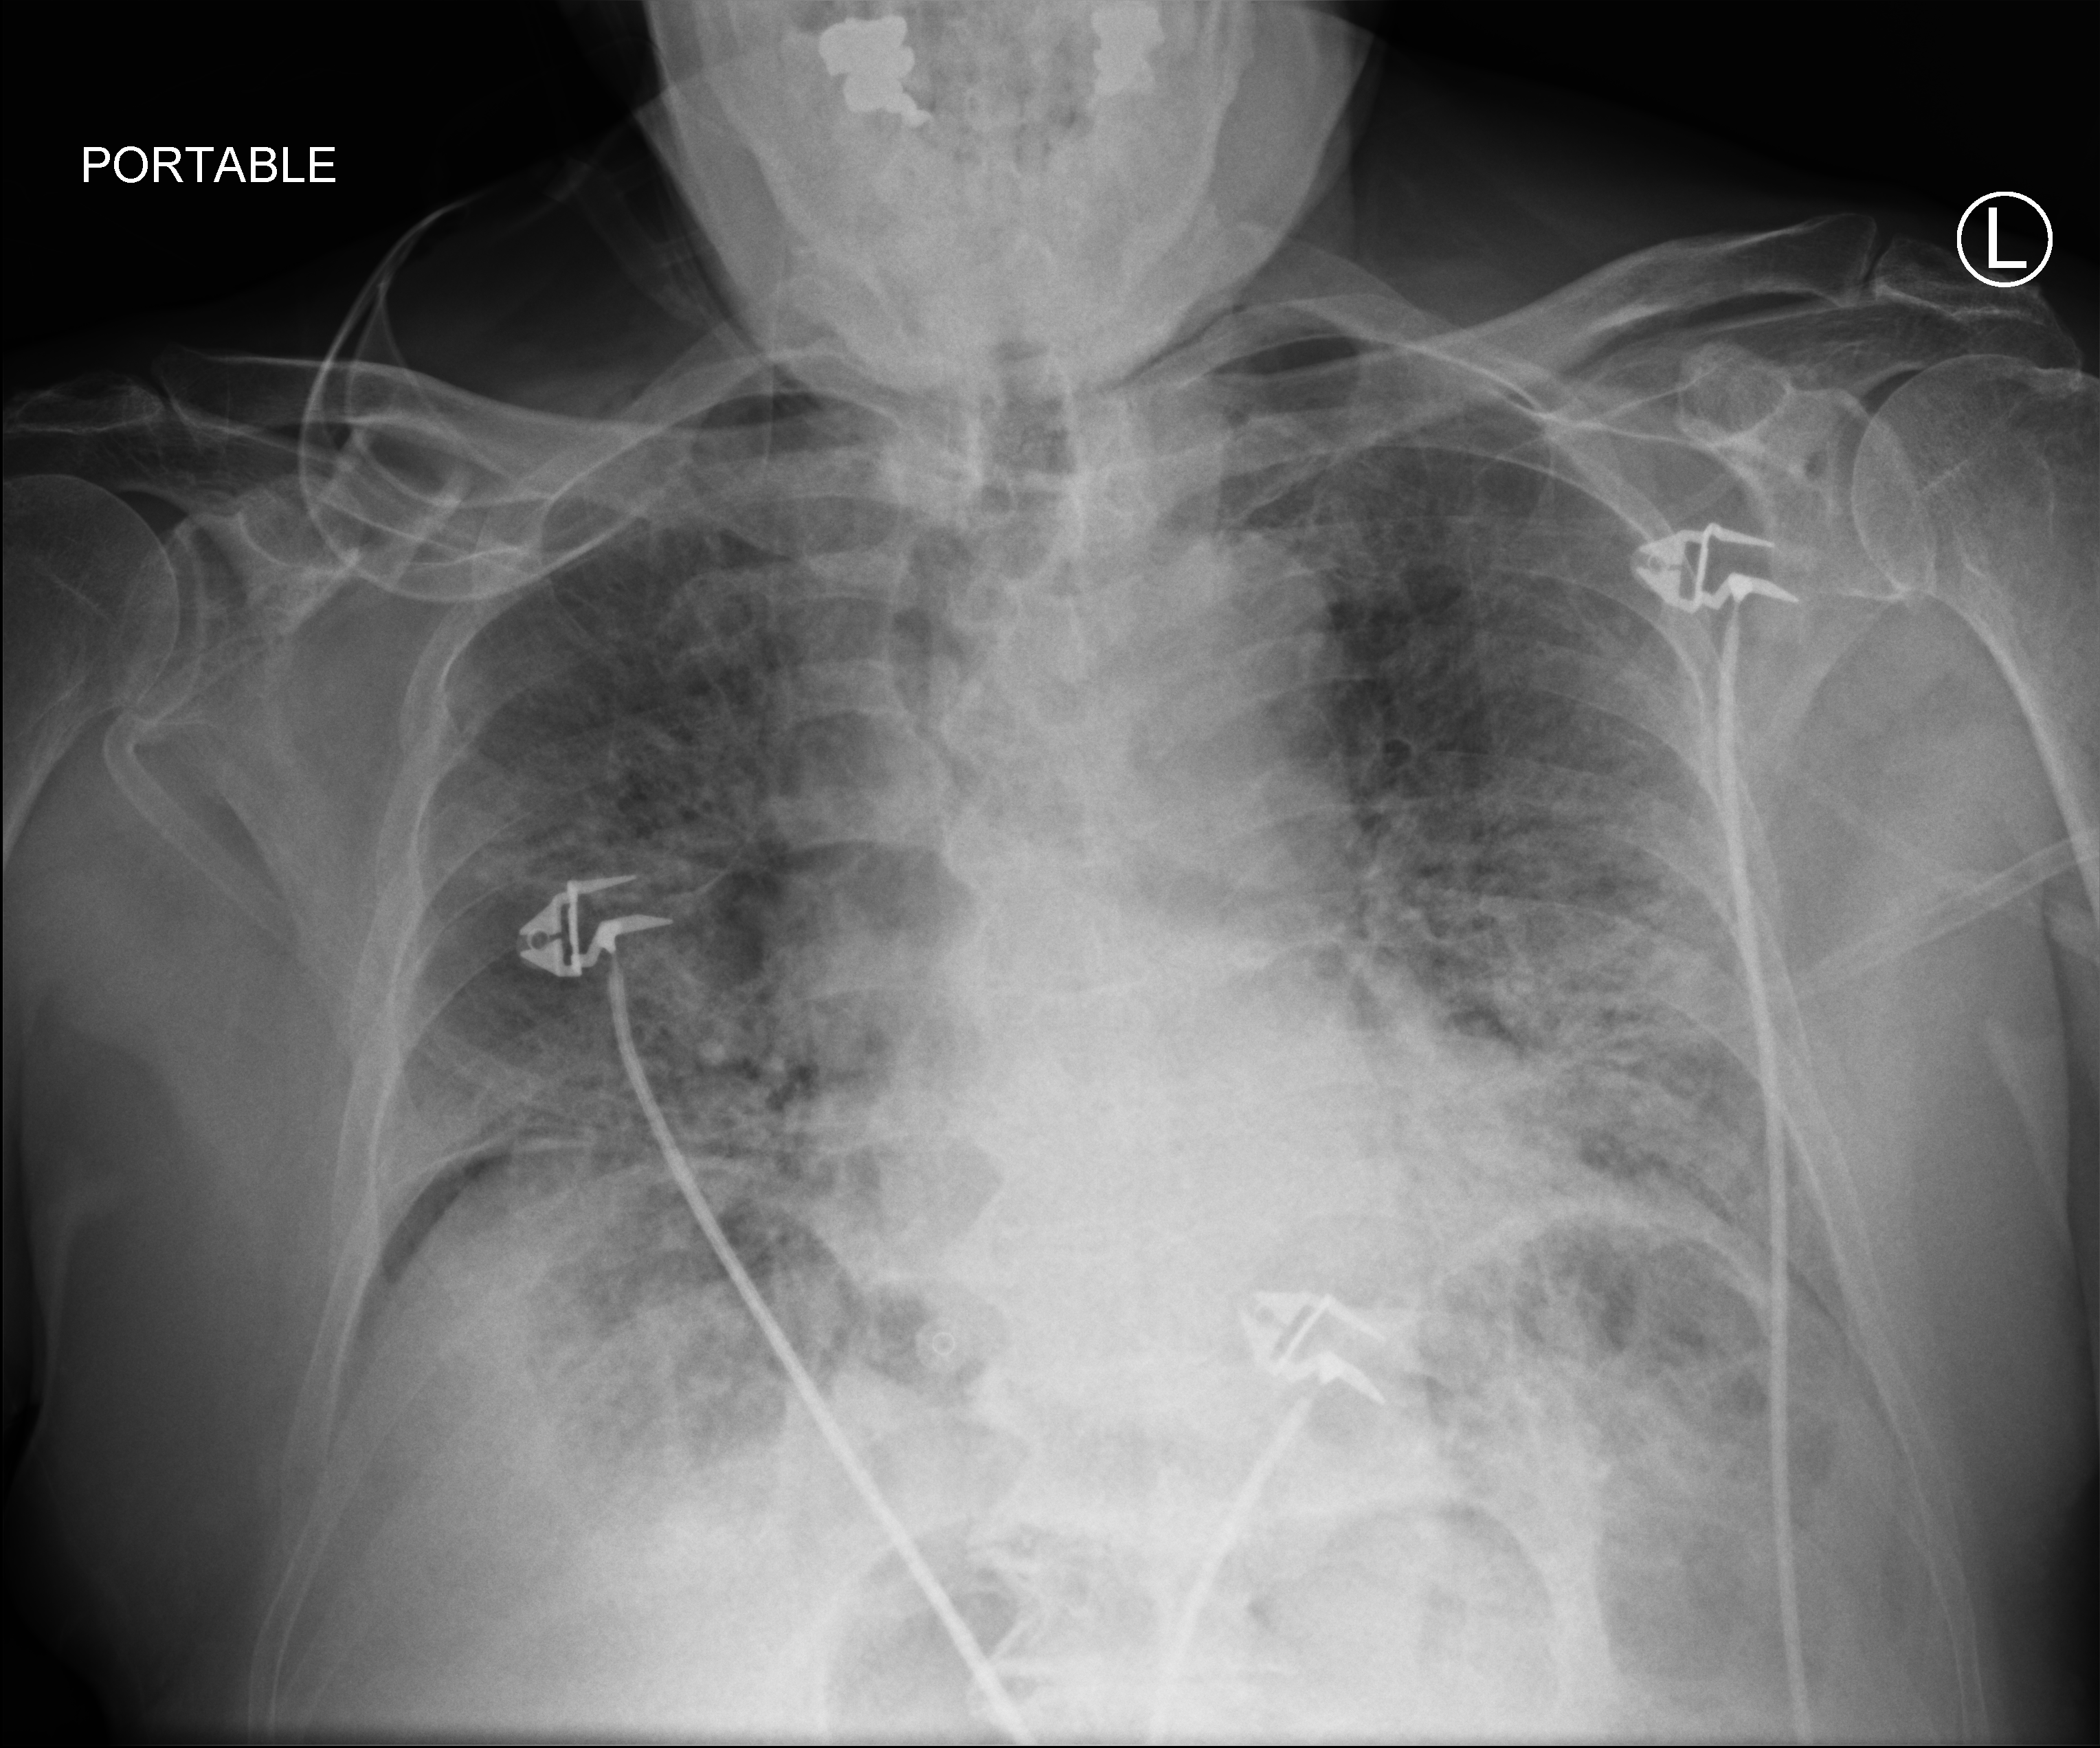
Bedside chest radiograph (computed radiography), anteroposterior (AP) projection. Male patient hospitalised with COVID-19, age 75–90 years.
Hospital-stay facts (about this admission, not read from this image; timing relative to this image not recorded): mechanically ventilated during this hospital stay: no.